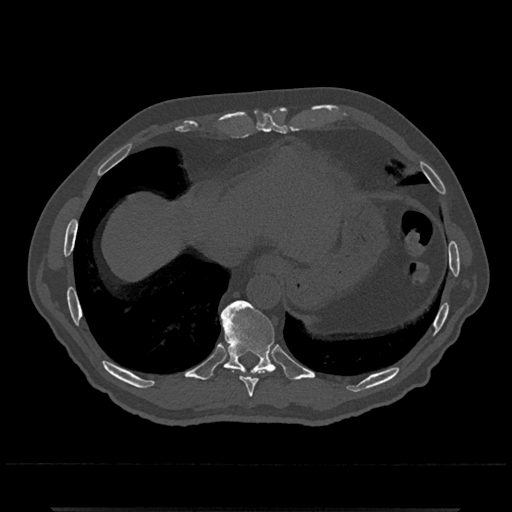
CT including the spine, one axial slice. Position 580 of 797 along the scan axis. Reconstruction kernel Br40s/3. Bone window (W 1800 / L 400 HU). 0.5 mm slice thickness. 512 × 512 image matrix, field of view 393 × 393 mm. Male patient, age 67 years. From the clinical record (not read from this slice): primary cancer: prostate.
Outlined on this slice (semi-automatically segmented with operator editing):
- T10 vertebra: box from (x=221, y=300) to (x=277, y=374) px
- T9 vertebra: (x=240, y=372)–(x=263, y=398)